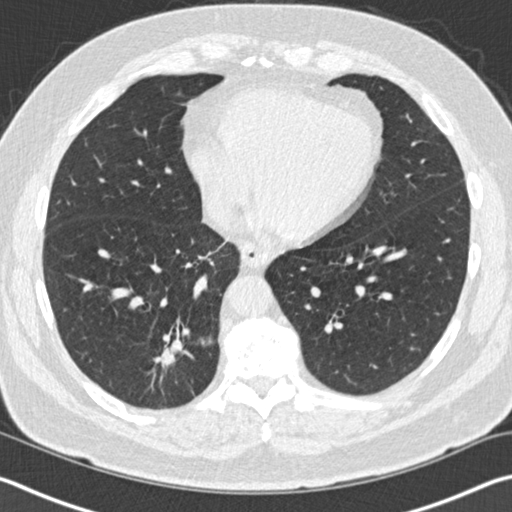
Low-dose screening chest CT, one axial slice; slice 39 of 141 in the series (ordered by position); reconstruction kernel B30f; lung window (W 1500 / L -600 HU); 2 mm slice thickness; 512 × 512 image matrix, field of view 344 × 344 mm.
Outlined on this slice (manually delineated by an expert):
- lesion 1 (tumor, lower lobe of right lung): bounding box <154,339,183,368> (left, top, right, bottom; pixels)